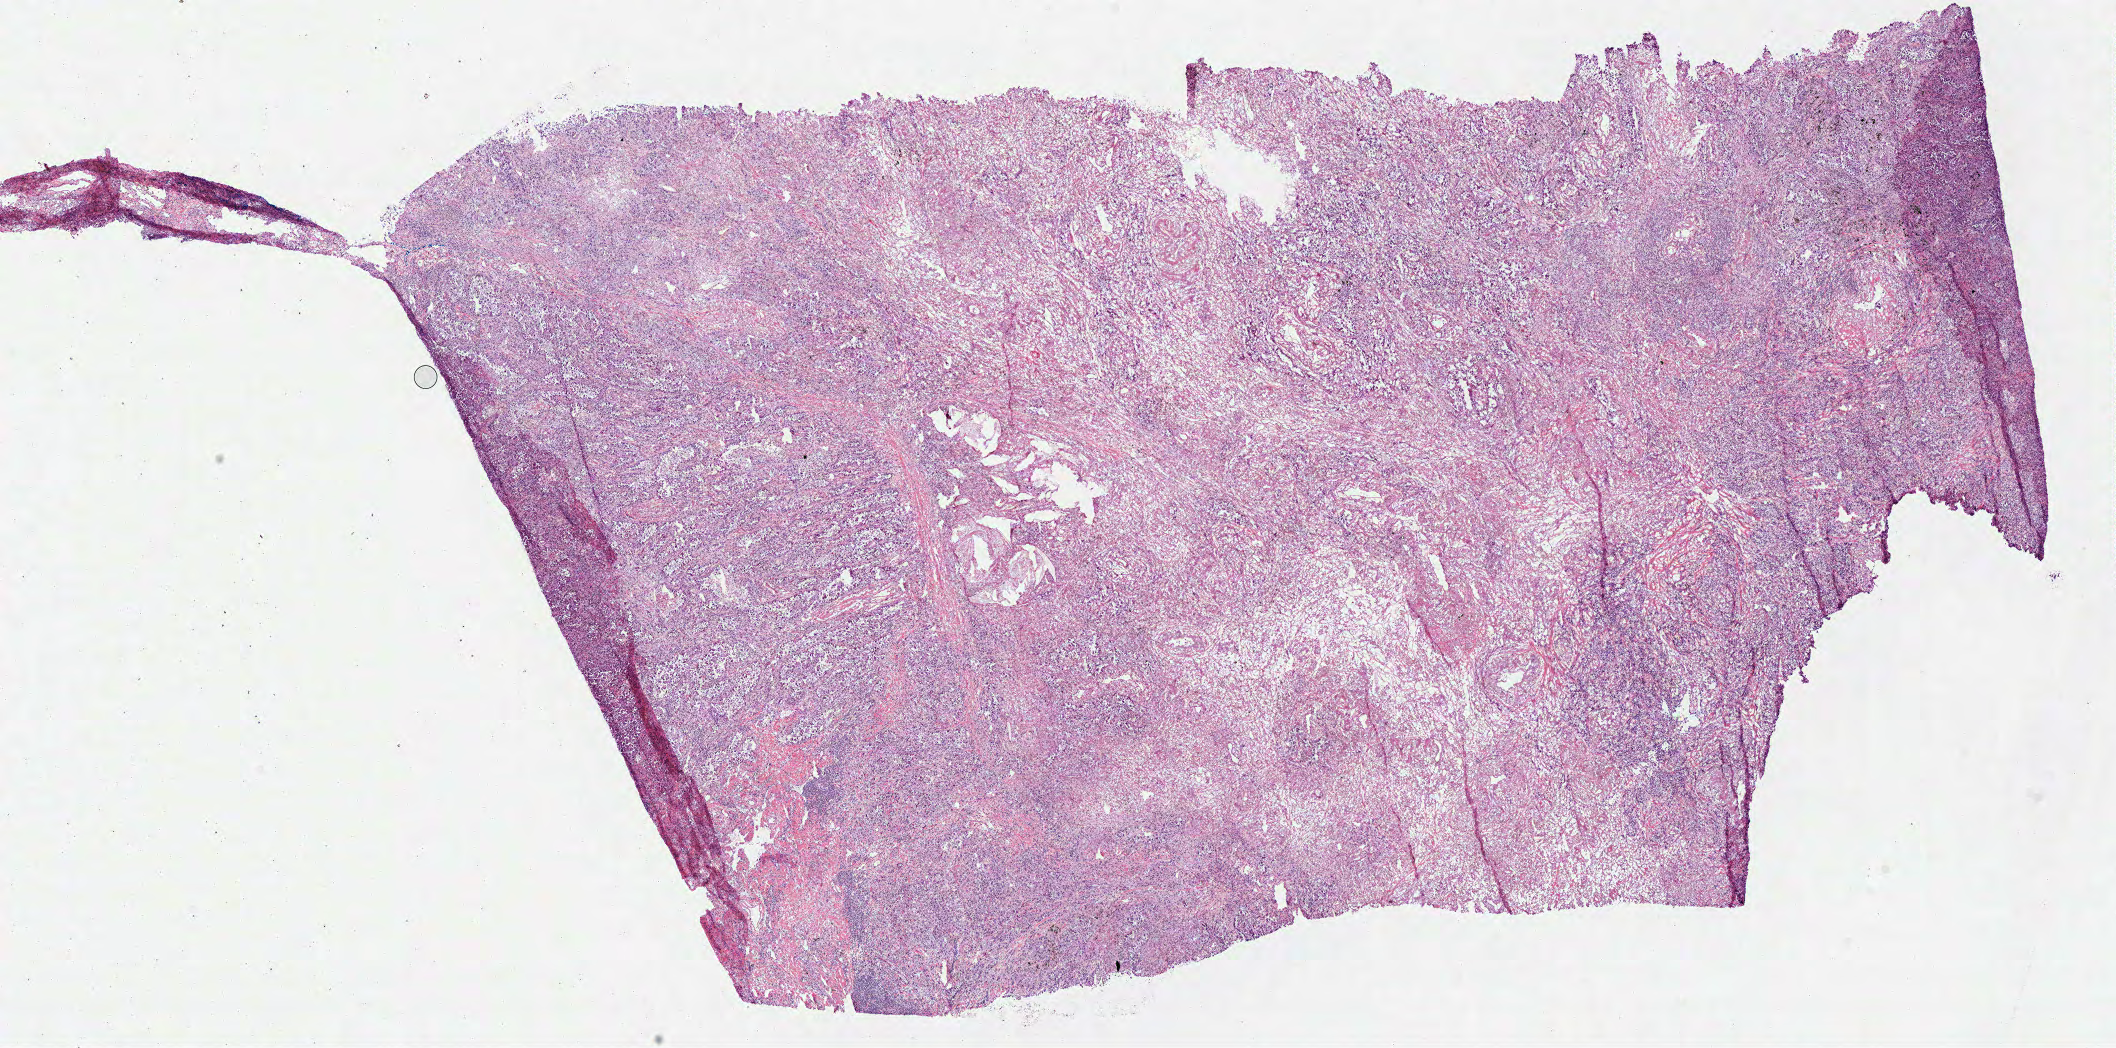
Whole-slide histology image, Hematoxylin and eosin (H&E) stained — shown as a low-resolution overview of the whole scanned area (about 16.6 x 8.2 mm), frozen section from the bottom of the tissue portion, sample: primary tumour, lung. Female, age 85 years at initial diagnosis. Slide review estimates, as recorded: tumour nuclei 65%, necrosis 0%. Inflammatory infiltration, as recorded: lymphocyte infiltration 20%, monocyte infiltration 0%, neutrophil infiltration 0%.
Diagnosis: Adenocarcinoma, NOS (upper lobe, lung). TNM: T2 NX MX. AJCC pathologic stage: IB (6th edition). Laterality: left.